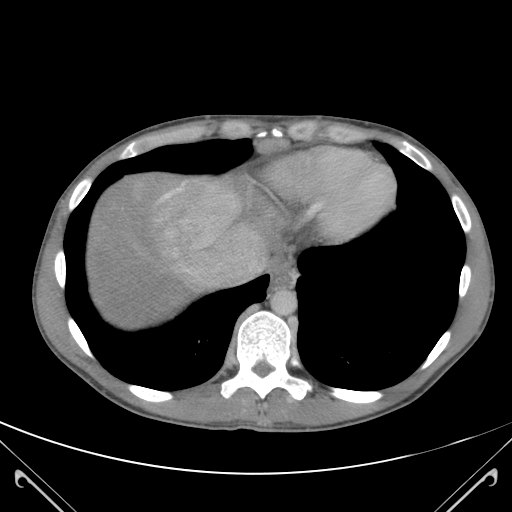
Contrast-enhanced abdominal CT (liver protocol), one axial slice; position 105 of 118 along the scan axis; 120 kVp; soft-tissue window (W 400 / L 40 HU); 3 mm slice thickness; 512 × 512 image matrix. From the clinical record (not read from this slice): diagnosis: hepatocellular carcinoma (patient treated with transarterial chemoembolisation; whether this scan precedes or follows treatment is not stated here); TNM stage (as recorded): Stage-IIIB; Child-Pugh class: A; tumour nodularity: uninodular.
Outlined on this slice (semi-automatic segmentation, software-assisted and operator-edited):
- abdominal aorta: bounding box [x1, y1, x2, y2] px = [273, 290, 296, 313]
- liver parenchyma outside the tumour (the mass and vessels are separate outlines, so this box may not span the whole liver): [88, 173, 267, 320]
- liver vessels: [160, 183, 236, 275]